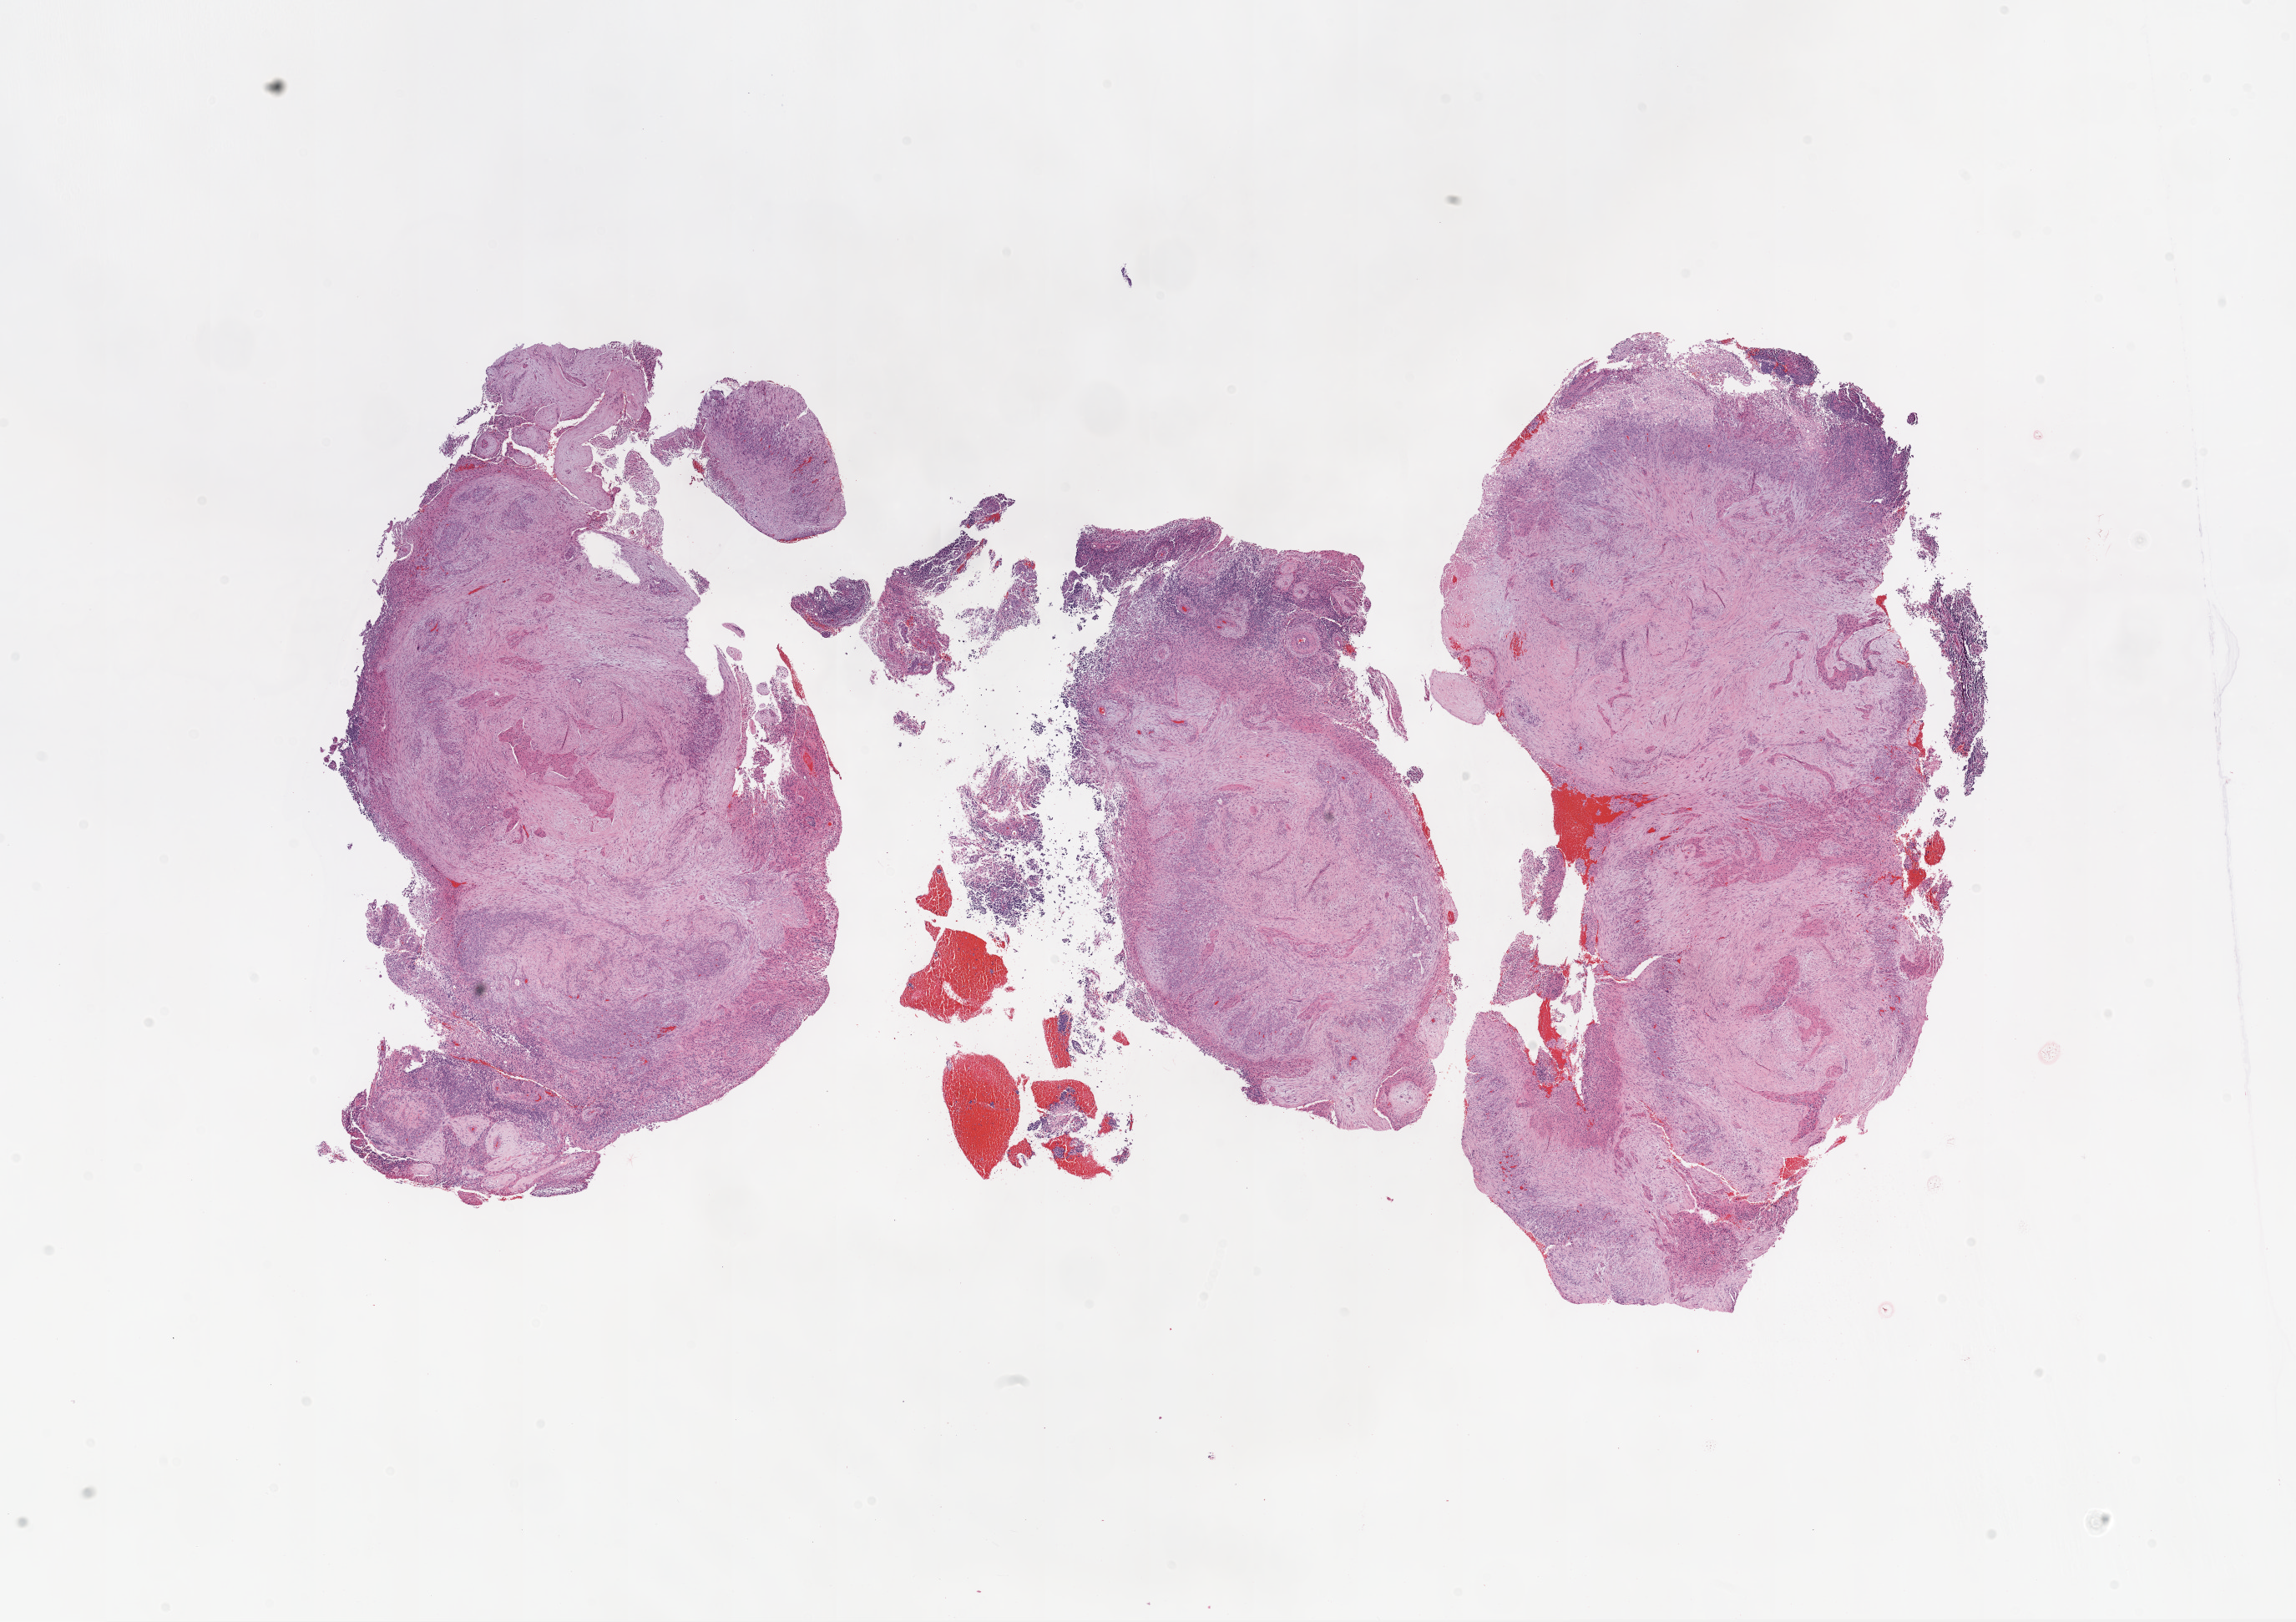
H&E-stained whole-slide image, whole scanned area (about 22.1 x 15.6 mm) shown as a low-resolution overview; FFPE section; primary tumour sample from the brain. Patient: male, age at initial diagnosis 61 years.
Diagnosis: Glioblastoma.